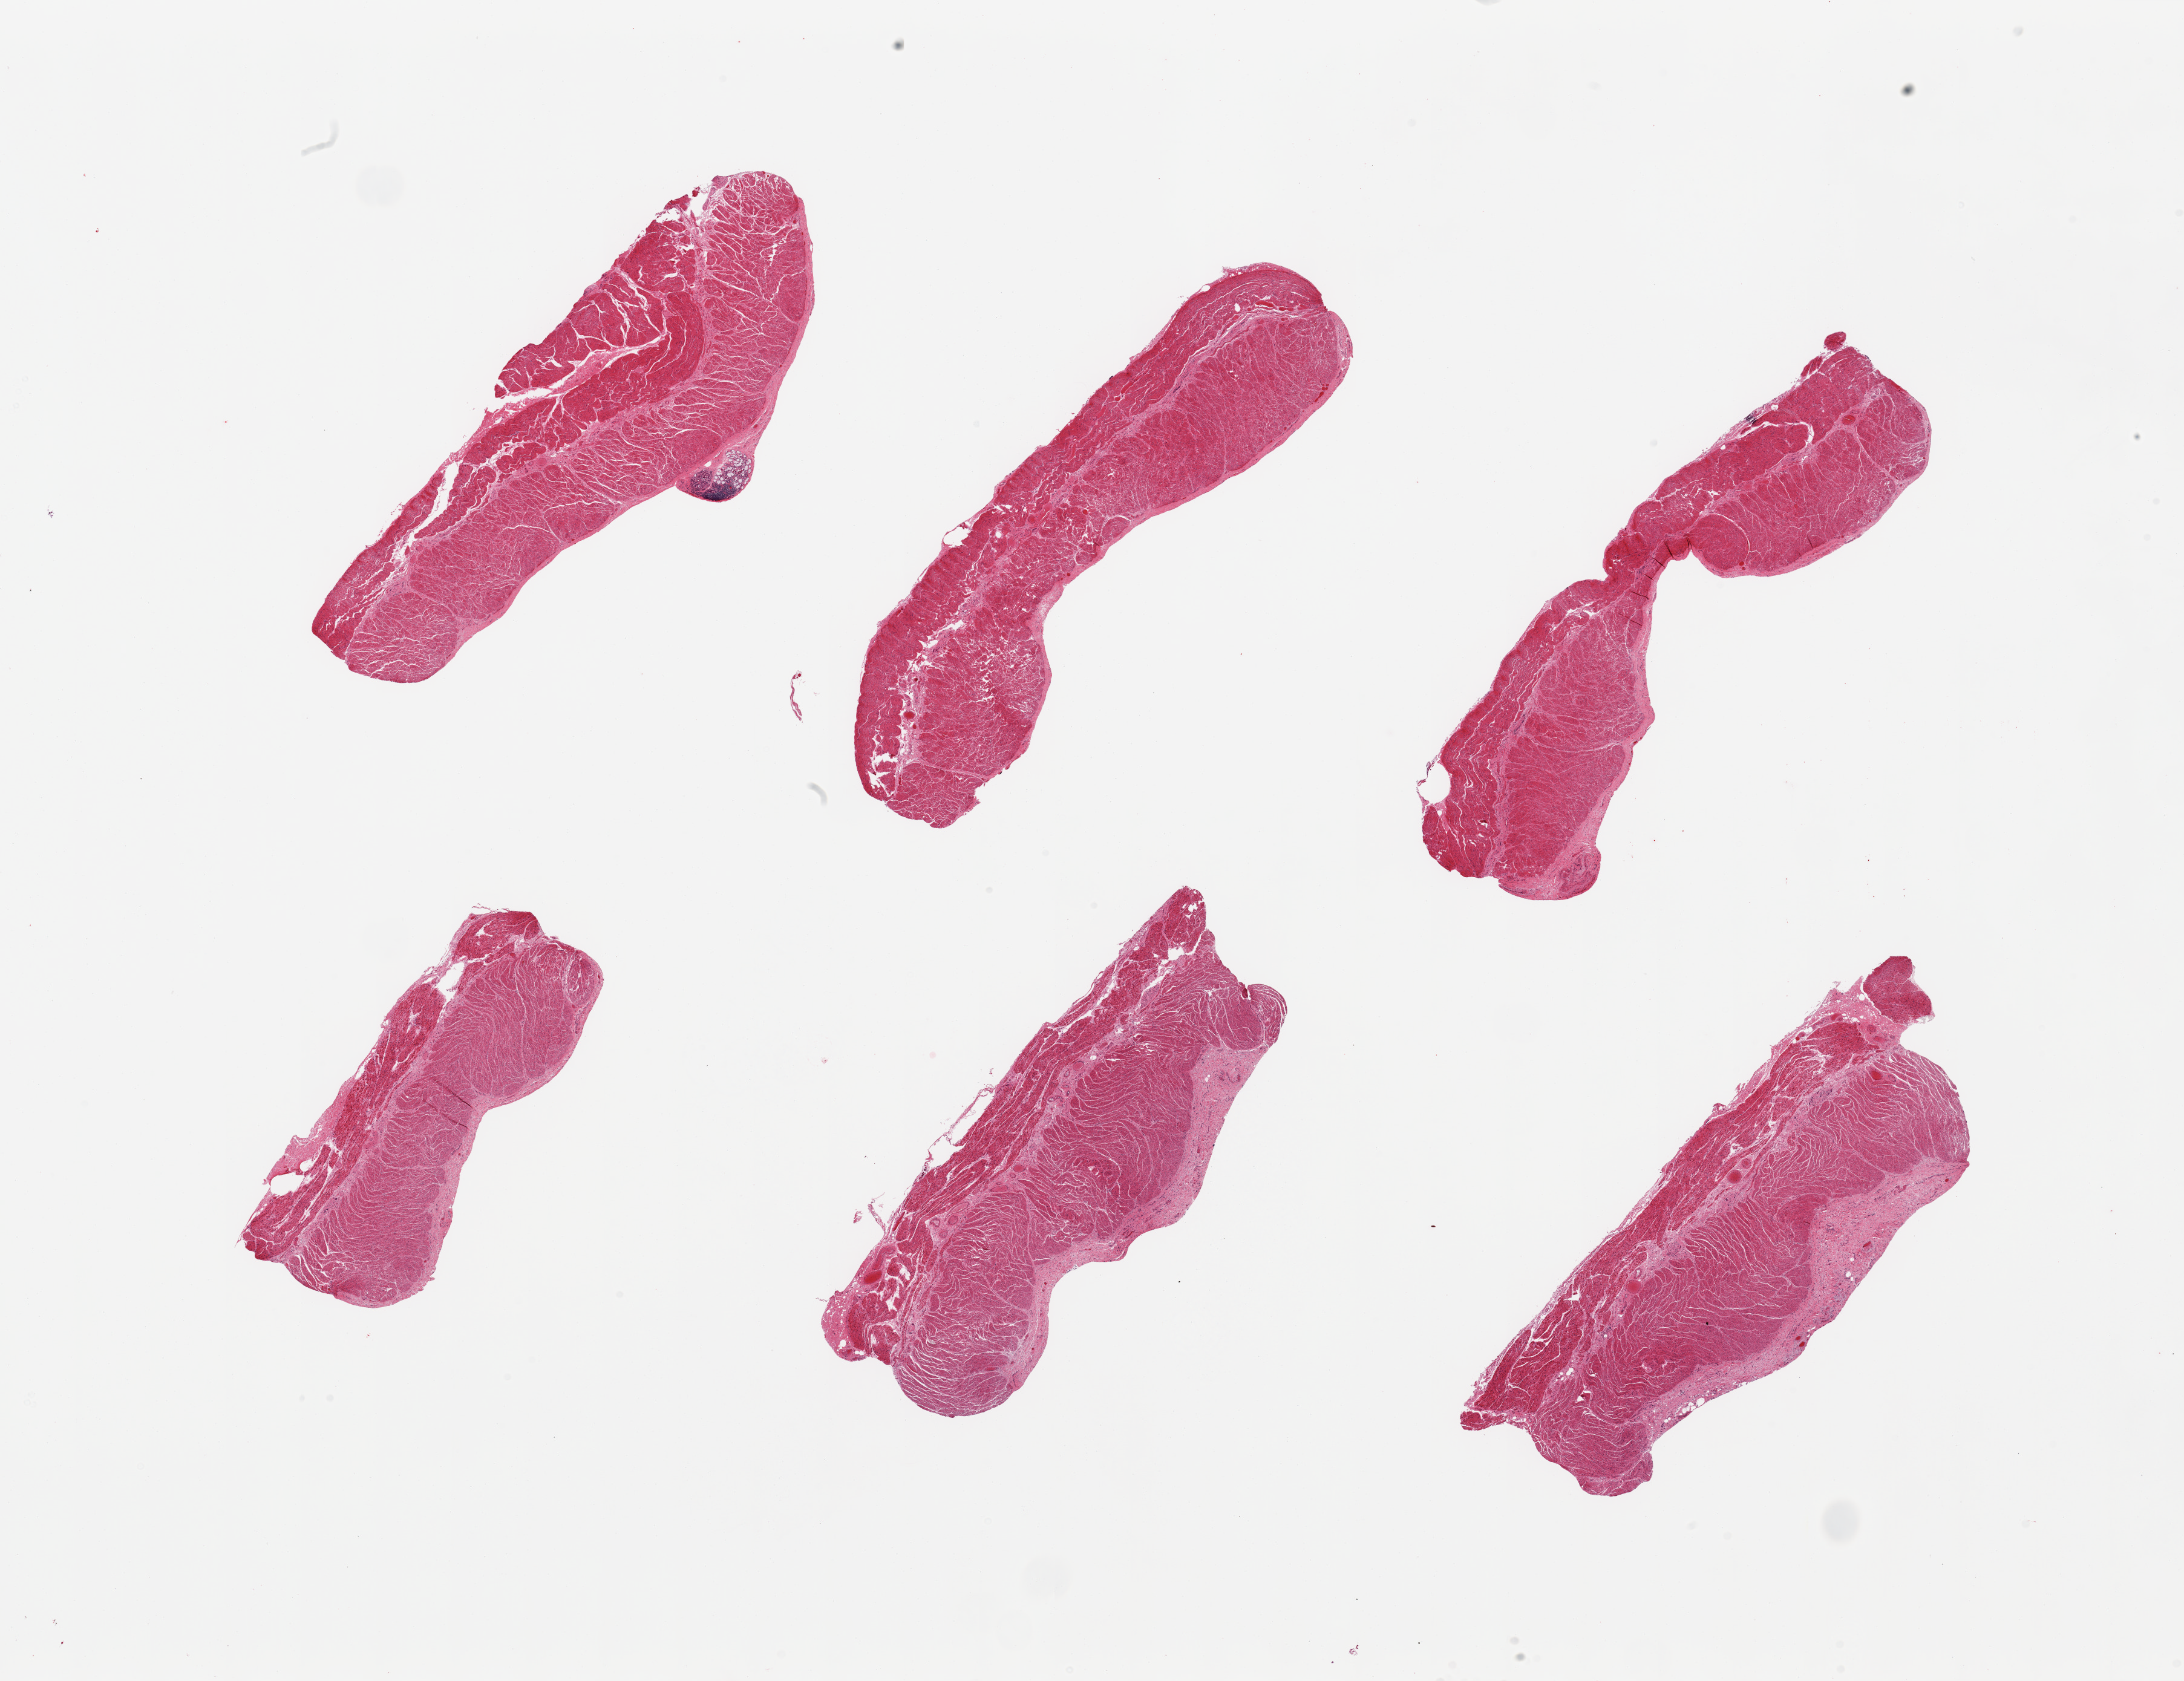
Digitized hematoxylin and eosin (H&E)-stained section, brightfield, low-resolution overview of the scanned area, about 28.5 x 22.0 mm (acquisition: 20x scan). PAXgene-fixed paraffin-embedded (PFPE) section. Target tissue: gastroesophageal junction. Donor tissue sample.
Pathologist's review note for this sample: 6 pieces; target muscularis with single tiny attachment of submucosal gland and lymphocytic infiltrate.